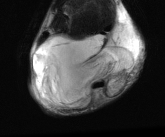
MRI of an extremity soft-tissue mass, one axial slice; slice 18 of 81 in the series (ordered by position); T2-weighted fat-saturated; MR volume resampled by the dataset authors to the PET/CT grid (not the native acquisition matrix); 3.27 mm slice thickness; 165 × 137 image matrix, field of view 161 × 134 mm. Male patient. From the clinical record (not read from this slice): histological type: liposarcoma - round cell; grade: high; site of the primary tumour: right calf.
Annotated regions visible in this slice (expert contour drawn on MRI and transferred to this co-registered scan by the dataset authors):
- gross tumour volume (mass): bounding box [x1, y1, x2, y2] px = [32, 25, 138, 110]